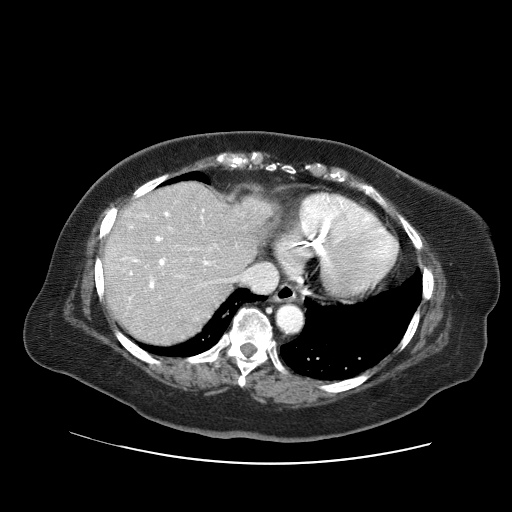
Contrast-enhanced abdominal CT (liver protocol), one axial slice; position 53 of 71 along the scan axis; 120 kVp; soft-tissue window (W 400 / L 40 HU); 2.5 mm slice thickness; 512 × 512 image matrix, field of view 400 × 400 mm. Case-level facts recorded for this patient, not image findings: diagnosis: hepatocellular carcinoma (patient treated with transarterial chemoembolisation; whether this scan precedes or follows treatment is not stated here); TNM stage (as recorded): Stage-II; Child-Pugh class: A.
Annotated regions visible in this slice (semi-automatically segmented with operator editing):
- liver parenchyma outside the tumour (the mass and vessels are separate outlines, so this box may not span the whole liver): bounding box <102,182,274,344> (left, top, right, bottom; pixels)
- liver vessels: <121,209,216,300>